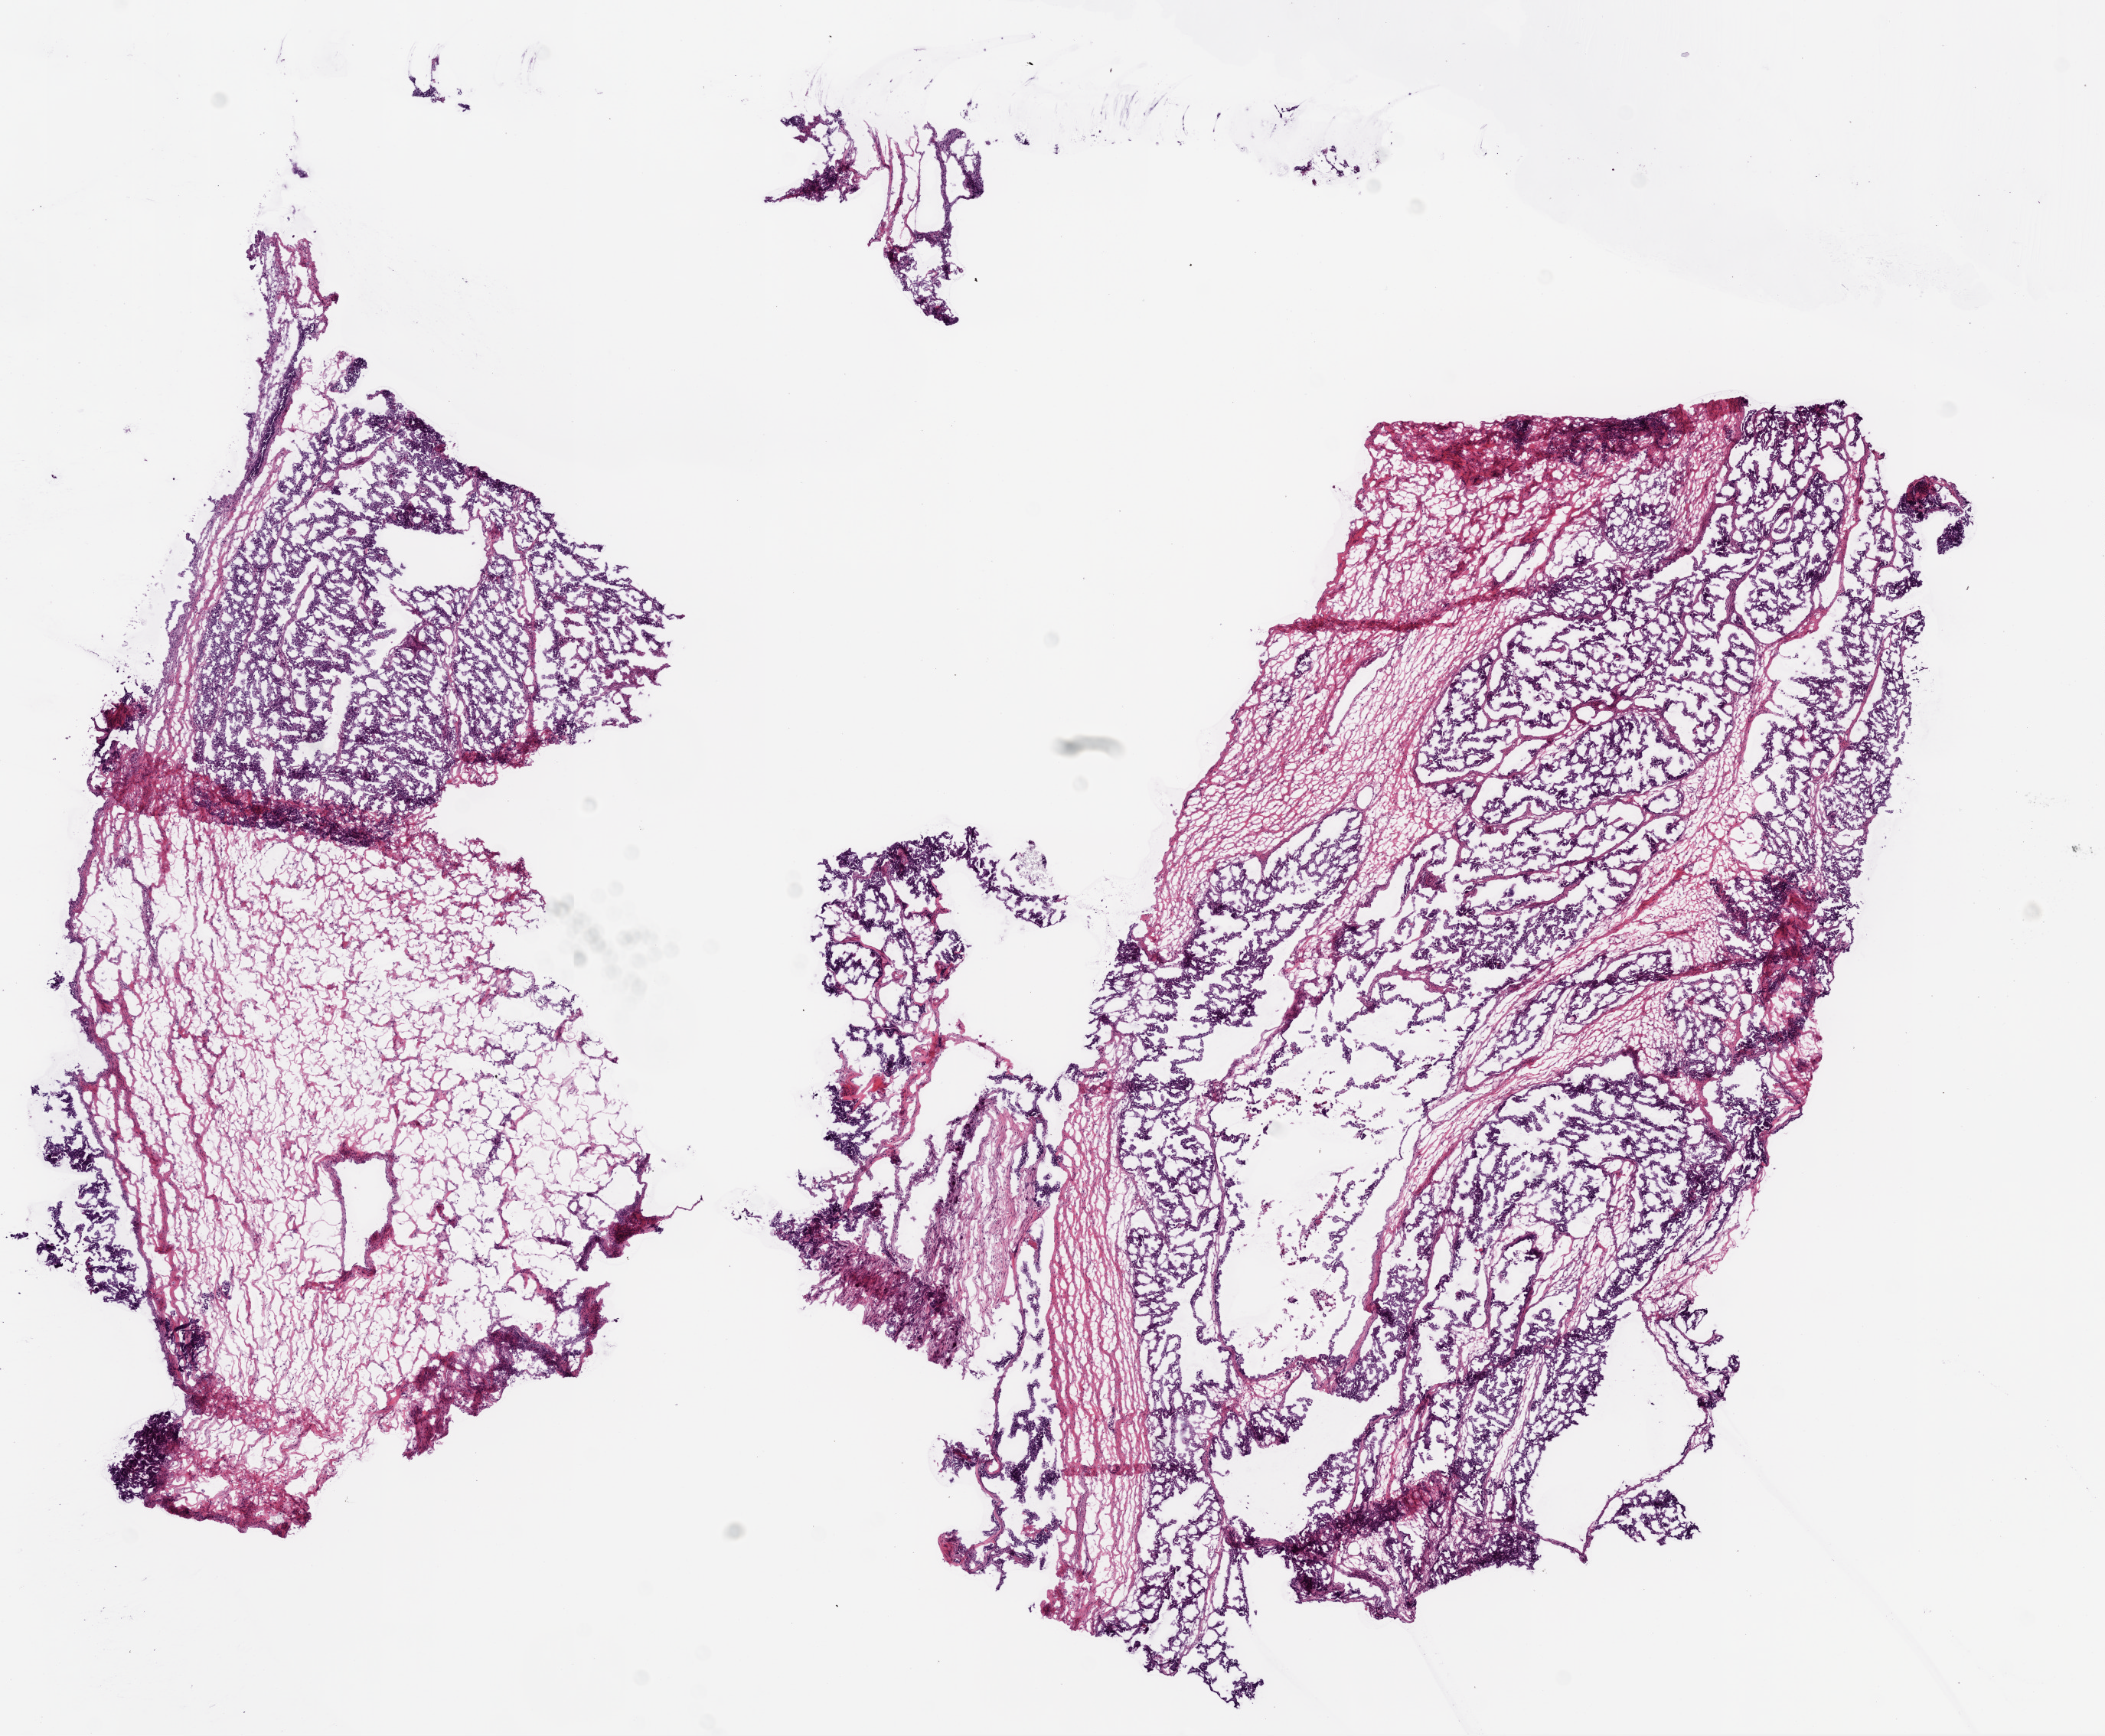
Digitized Hematoxylin and eosin (H&E) stained tissue section (whole slide), low-resolution overview of the scanned area, about 11.0 x 9.1 mm. Frozen section from the bottom of the tissue portion. Ovary, primary tumour sample. Female, age 47 years at initial diagnosis. Histologic grade: G3 (poorly differentiated). Pathologist review of this section (percent, as recorded): tumour cells 50%, tumour nuclei 70%, normal cells 0%, stromal cells 50%, necrosis 0%.
Laterality: bilateral. Diagnosis: Serous cystadenocarcinoma, NOS. FIGO stage: IIIC.